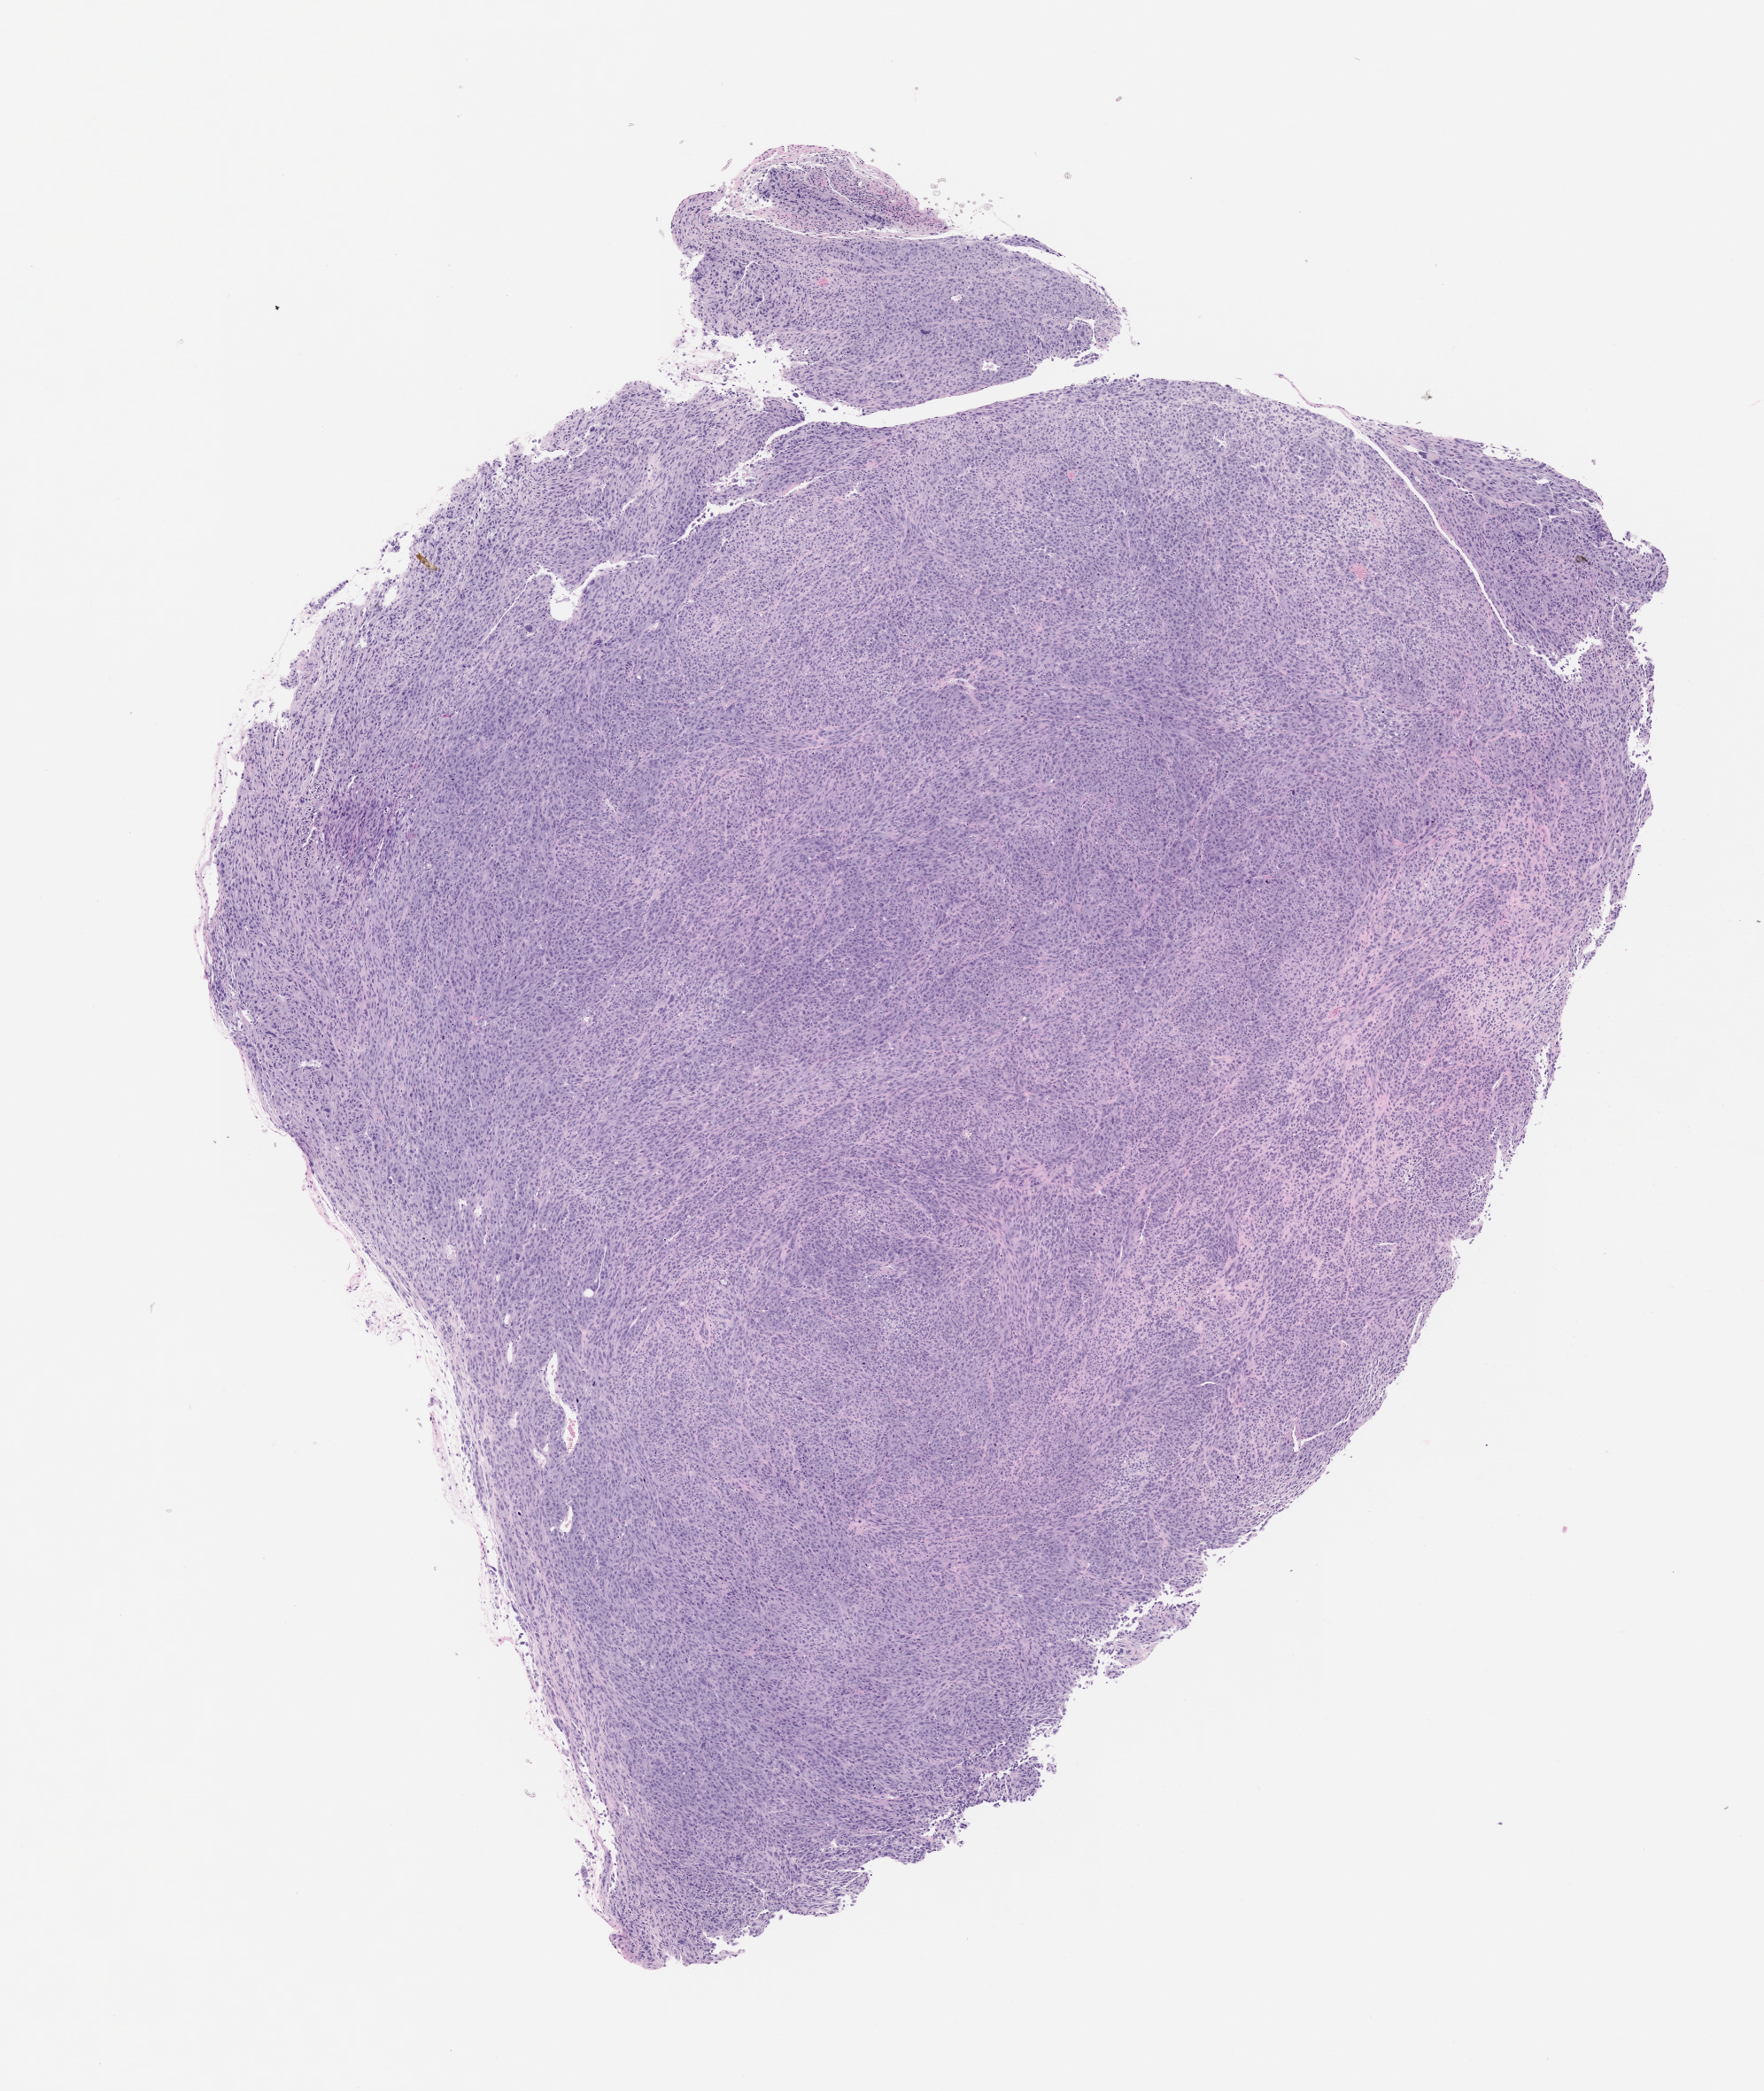
Hematoxylin and eosin (H&E) whole-slide image of a patient-derived xenograft (PDX) tumor grown in a mouse, passage 1 — a low-resolution overview of the entire scanned area, about 8.0 x 9.5 mm. FFPE section. Originating tumor site category: bone.
Originating patient diagnosis: Osteosarcoma.